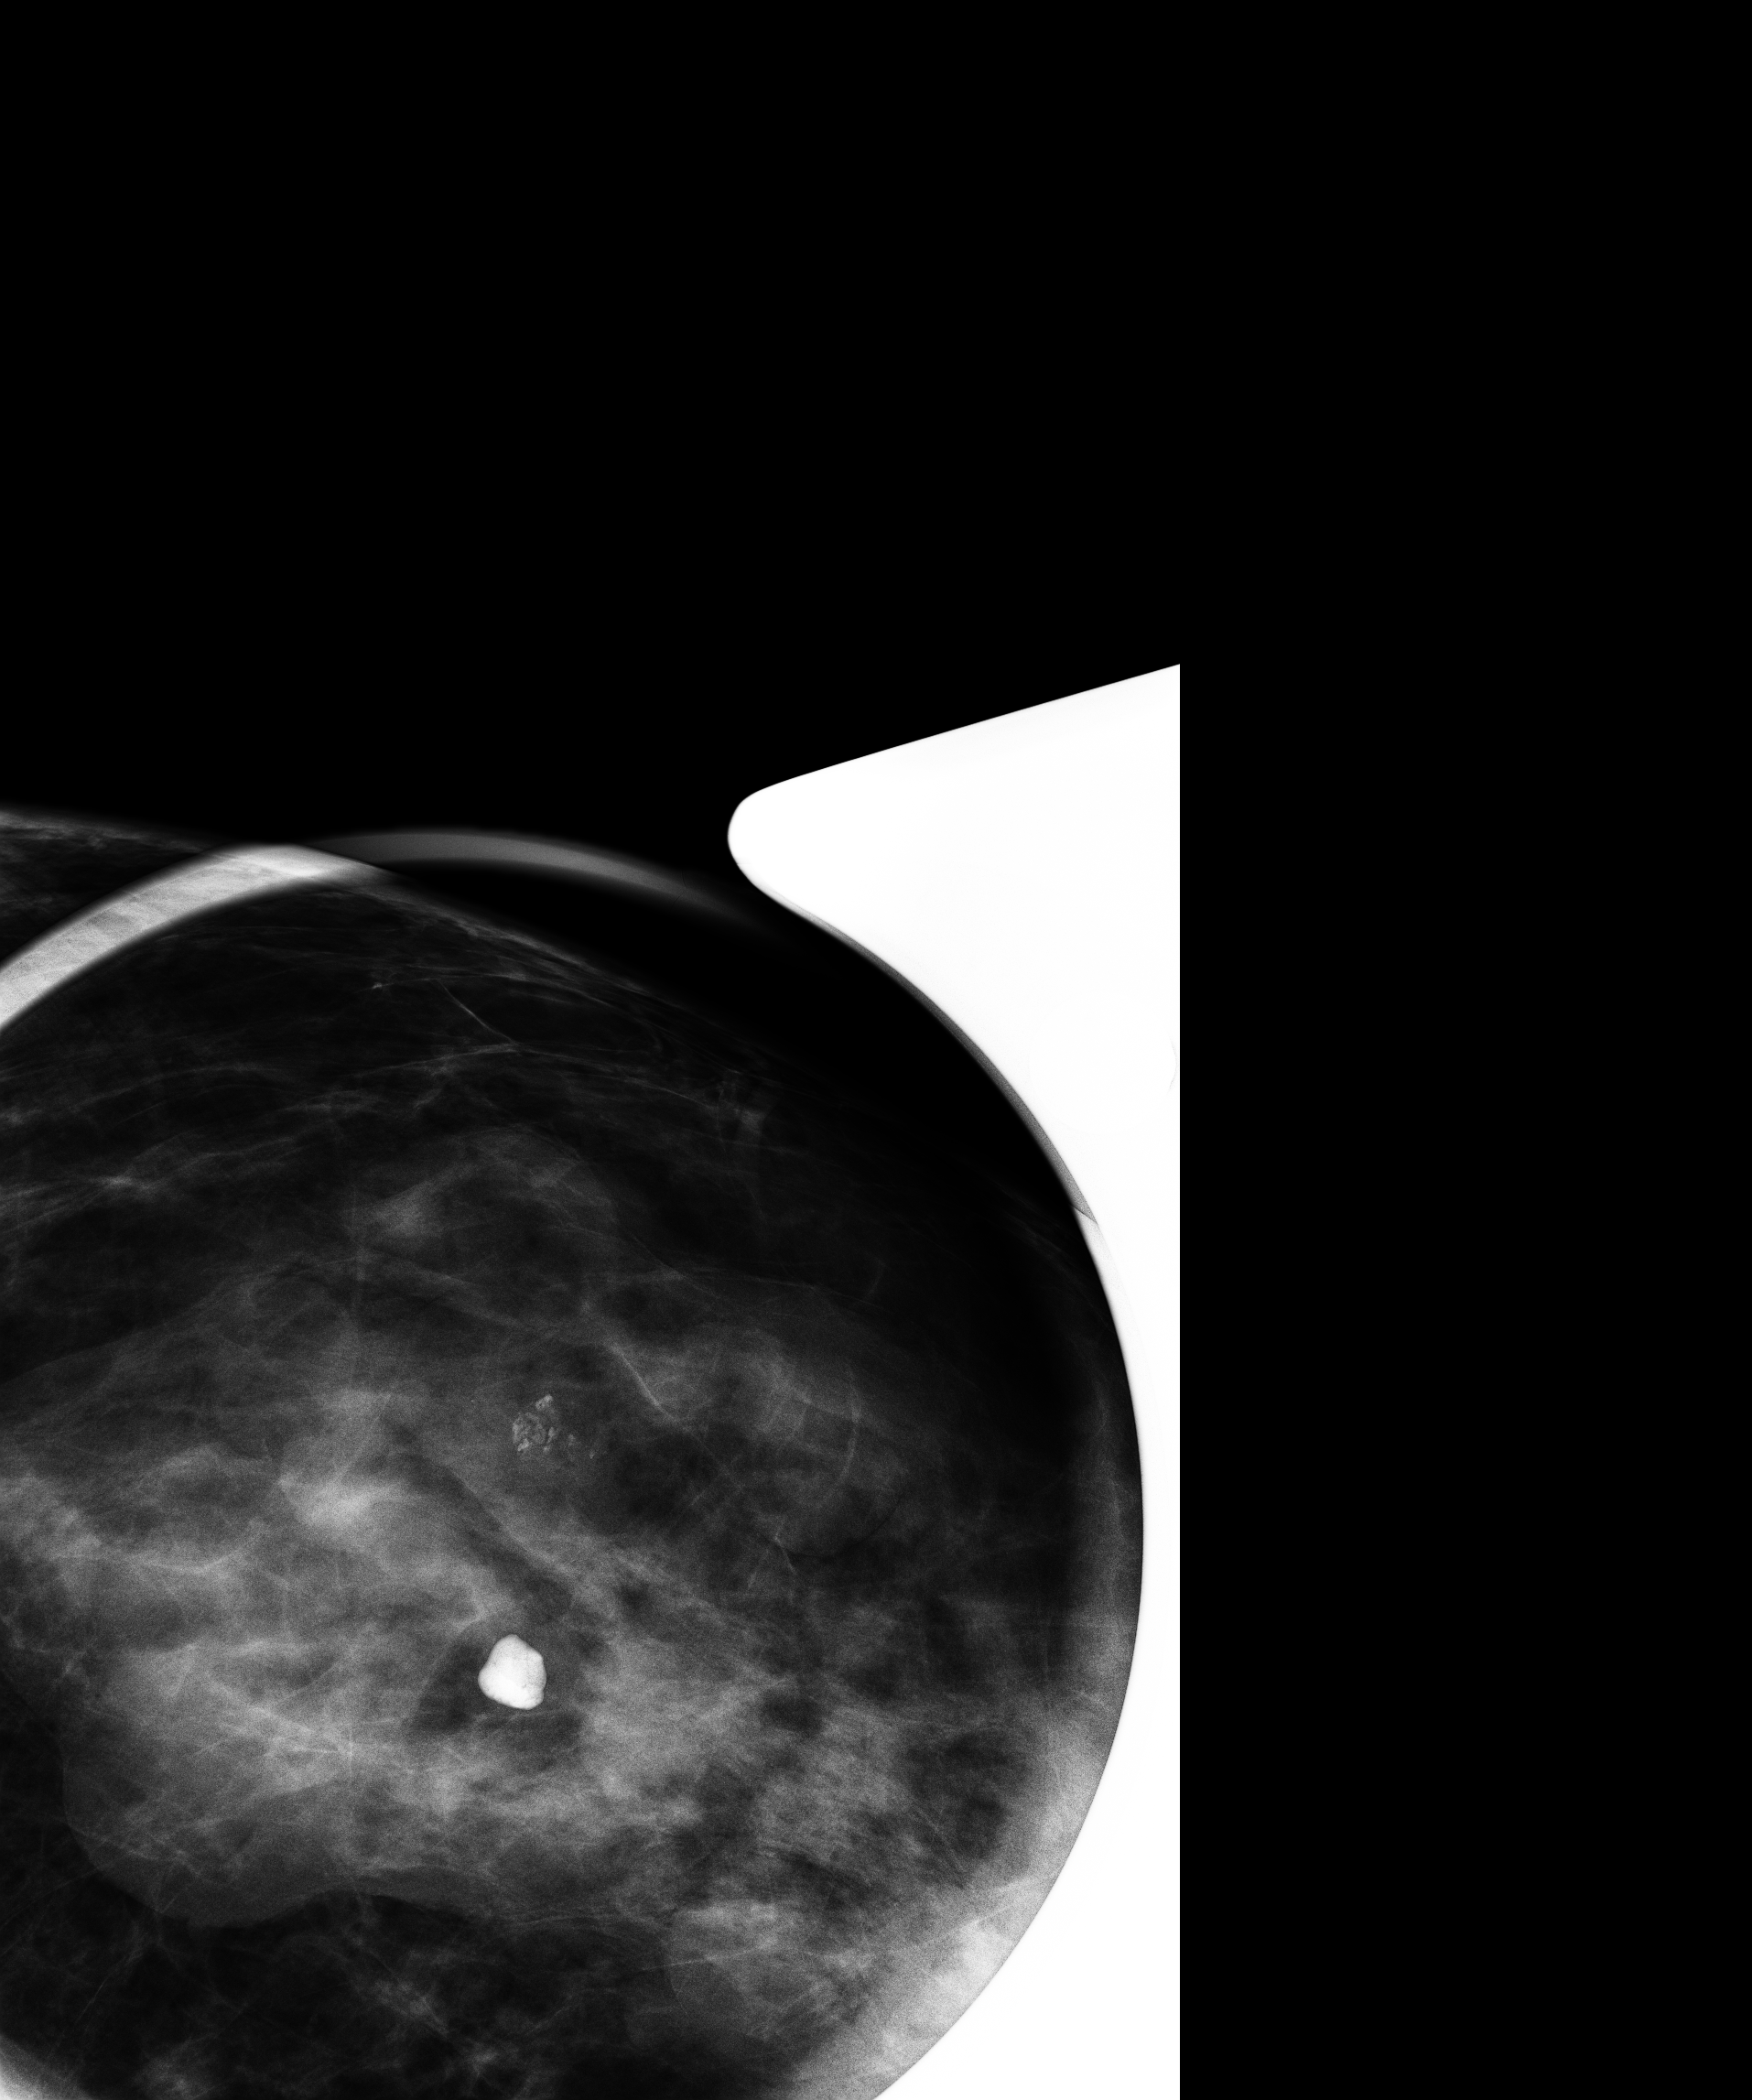
Diagnostic work-up study. Female patient, age 52 years.
Image type: full-field digital mammogram. Breast: left. Projection: craniocaudal (CC) view.